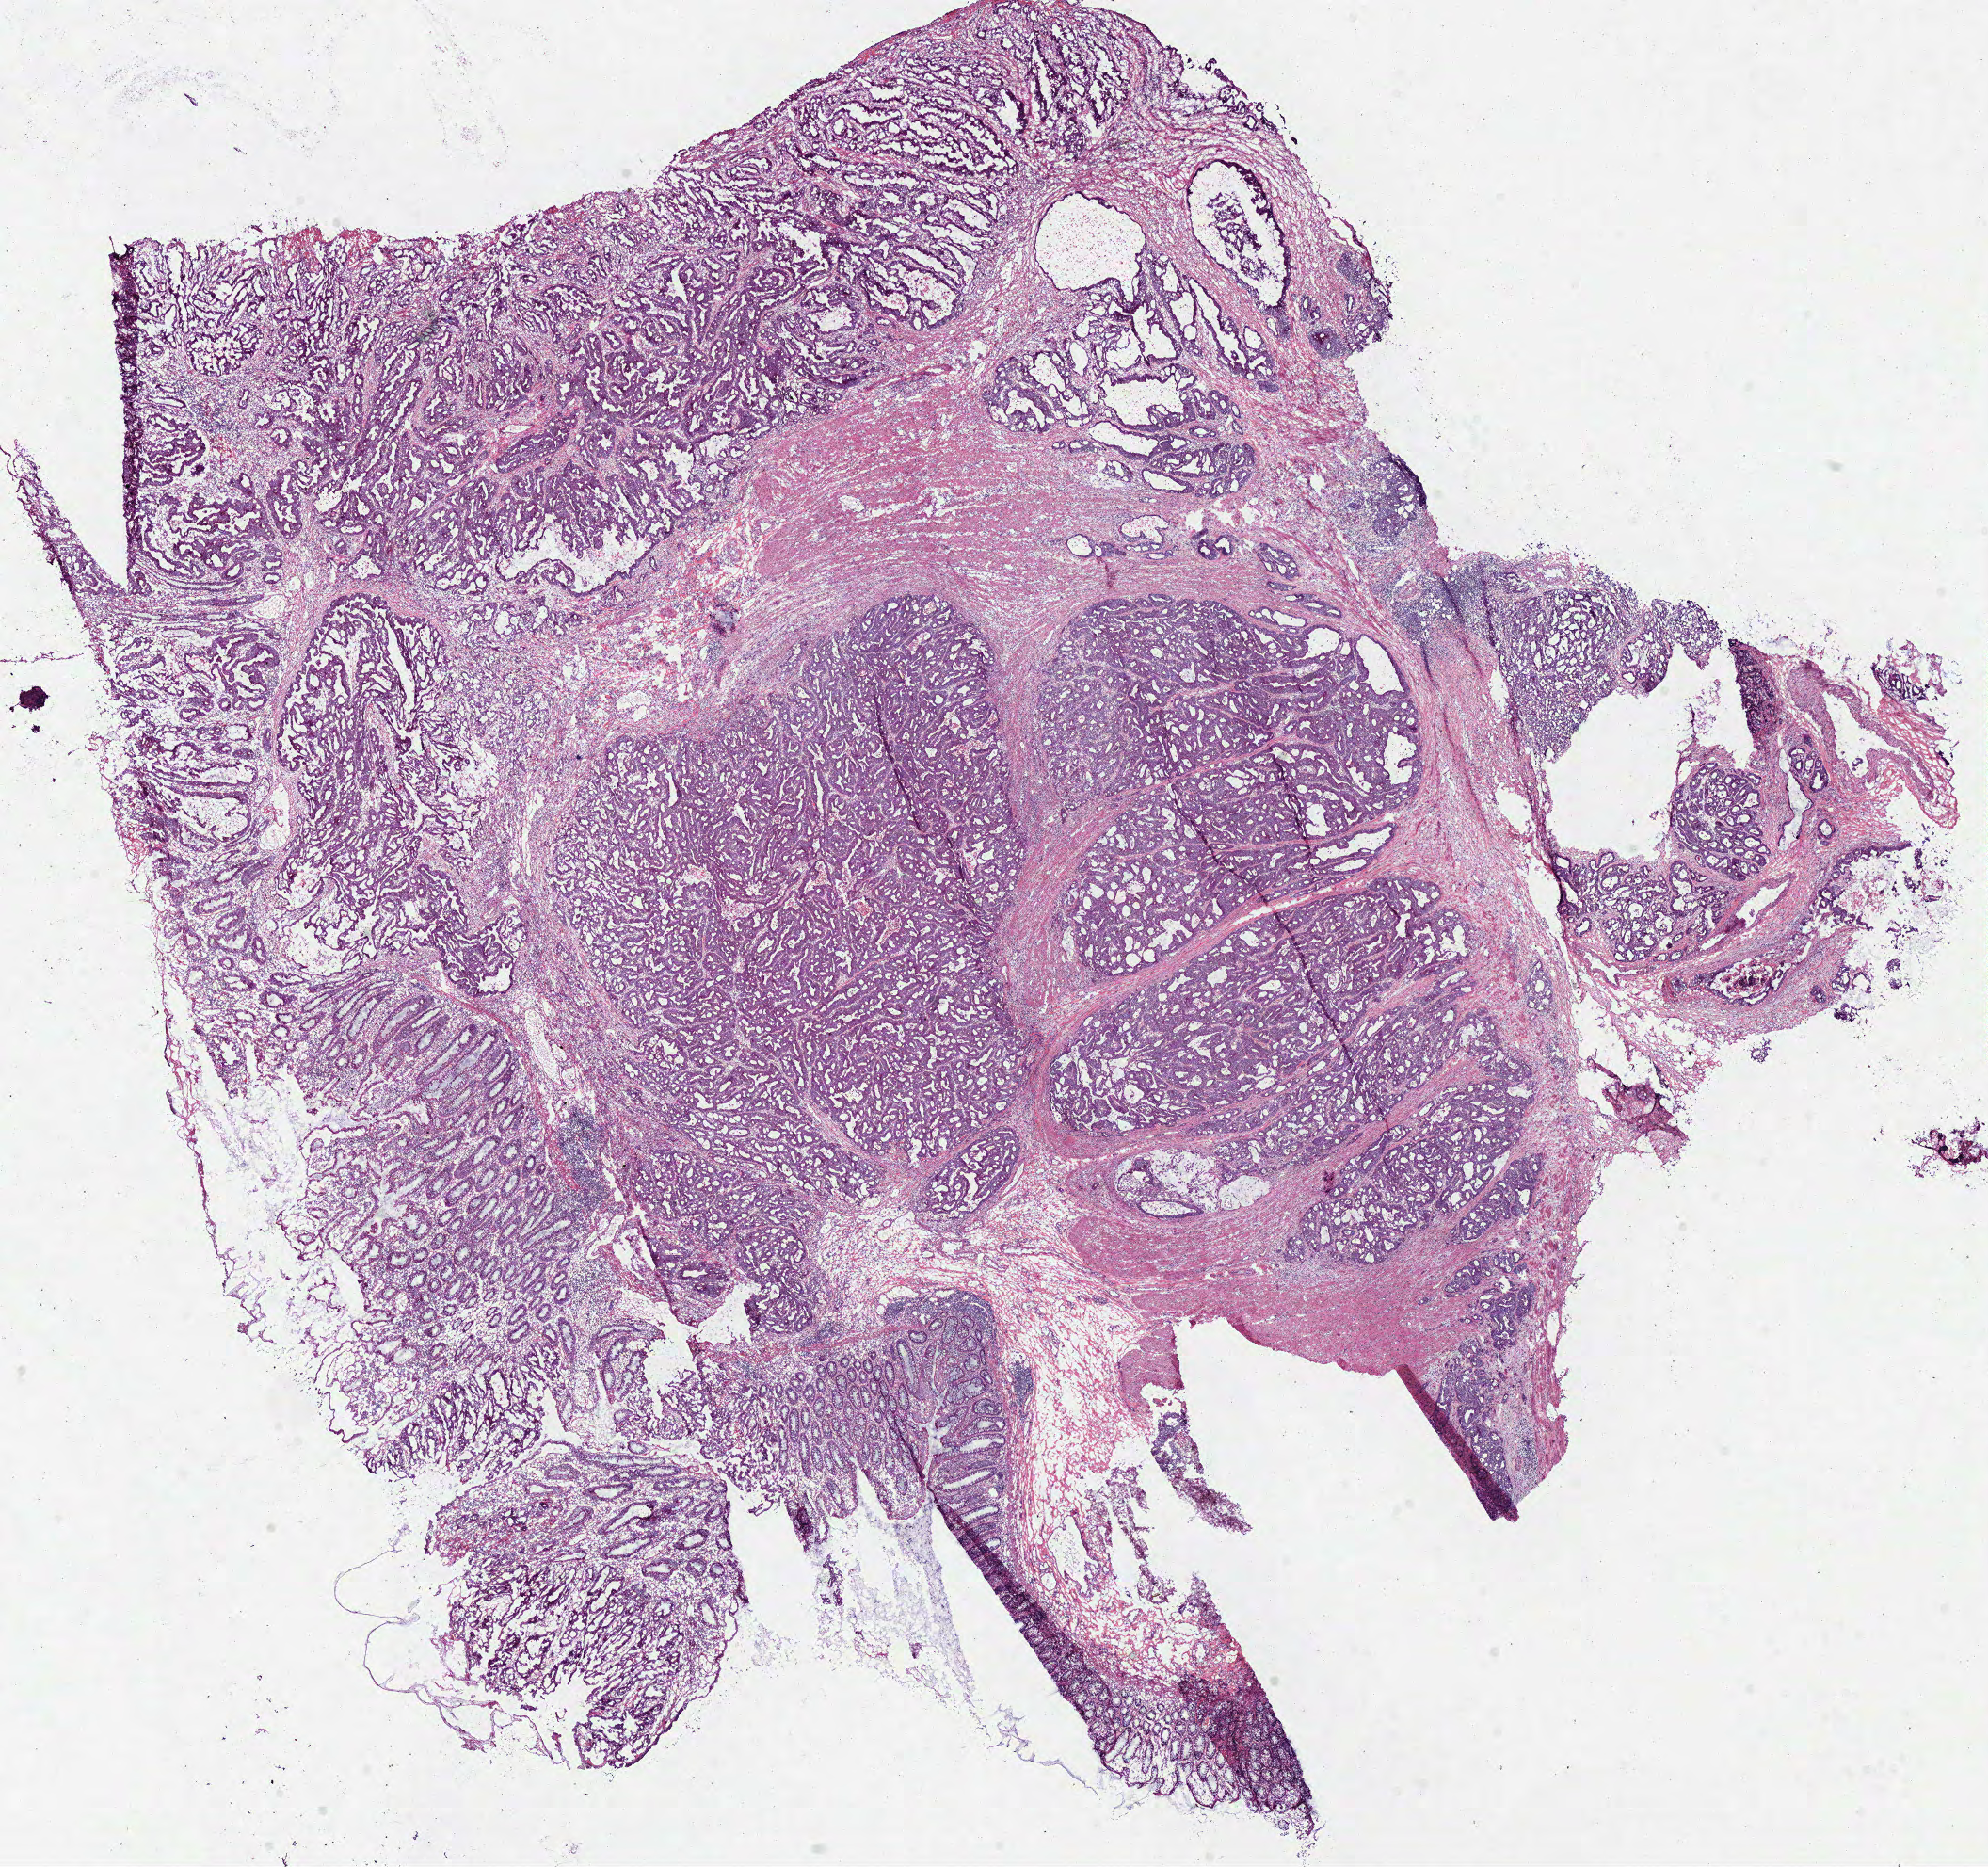
Digitized H&E tissue section (whole slide), whole scanned area (about 16.6 x 15.6 mm, from a 40x scan) shown as a low-resolution overview, frozen section from the bottom of the tissue portion, sample: primary tumour, colon. Patient: female, age at initial diagnosis 52 years. Pathologist review of this section (percent, as recorded): tumour cells 70%, tumour nuclei 80%, normal cells 10%, stromal cells 15%, necrosis 5%.
Histologic diagnosis: Adenocarcinoma, NOS (sigmoid colon). AJCC pathologic stage: IVA.